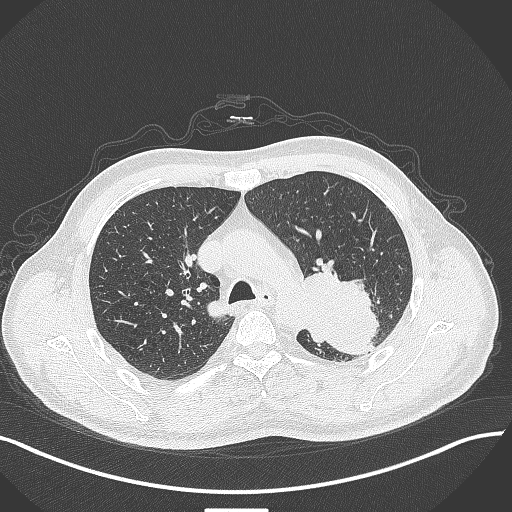
Chest CT, one axial slice. Lung window (W 1500 / L -600 HU). 1 mm slice thickness. 512 × 512 image matrix, field of view 400 × 400 mm. Patient: male, 55 years. From the clinical record (not read from this slice): clinical TNM (as recorded): T3 N0 M1c.
Outlined on this slice (rectangle marked by the reading radiologist):
- lung tumour (recorded histology: adenocarcinoma): bounding box <293,265,384,363> (left, top, right, bottom; pixels)